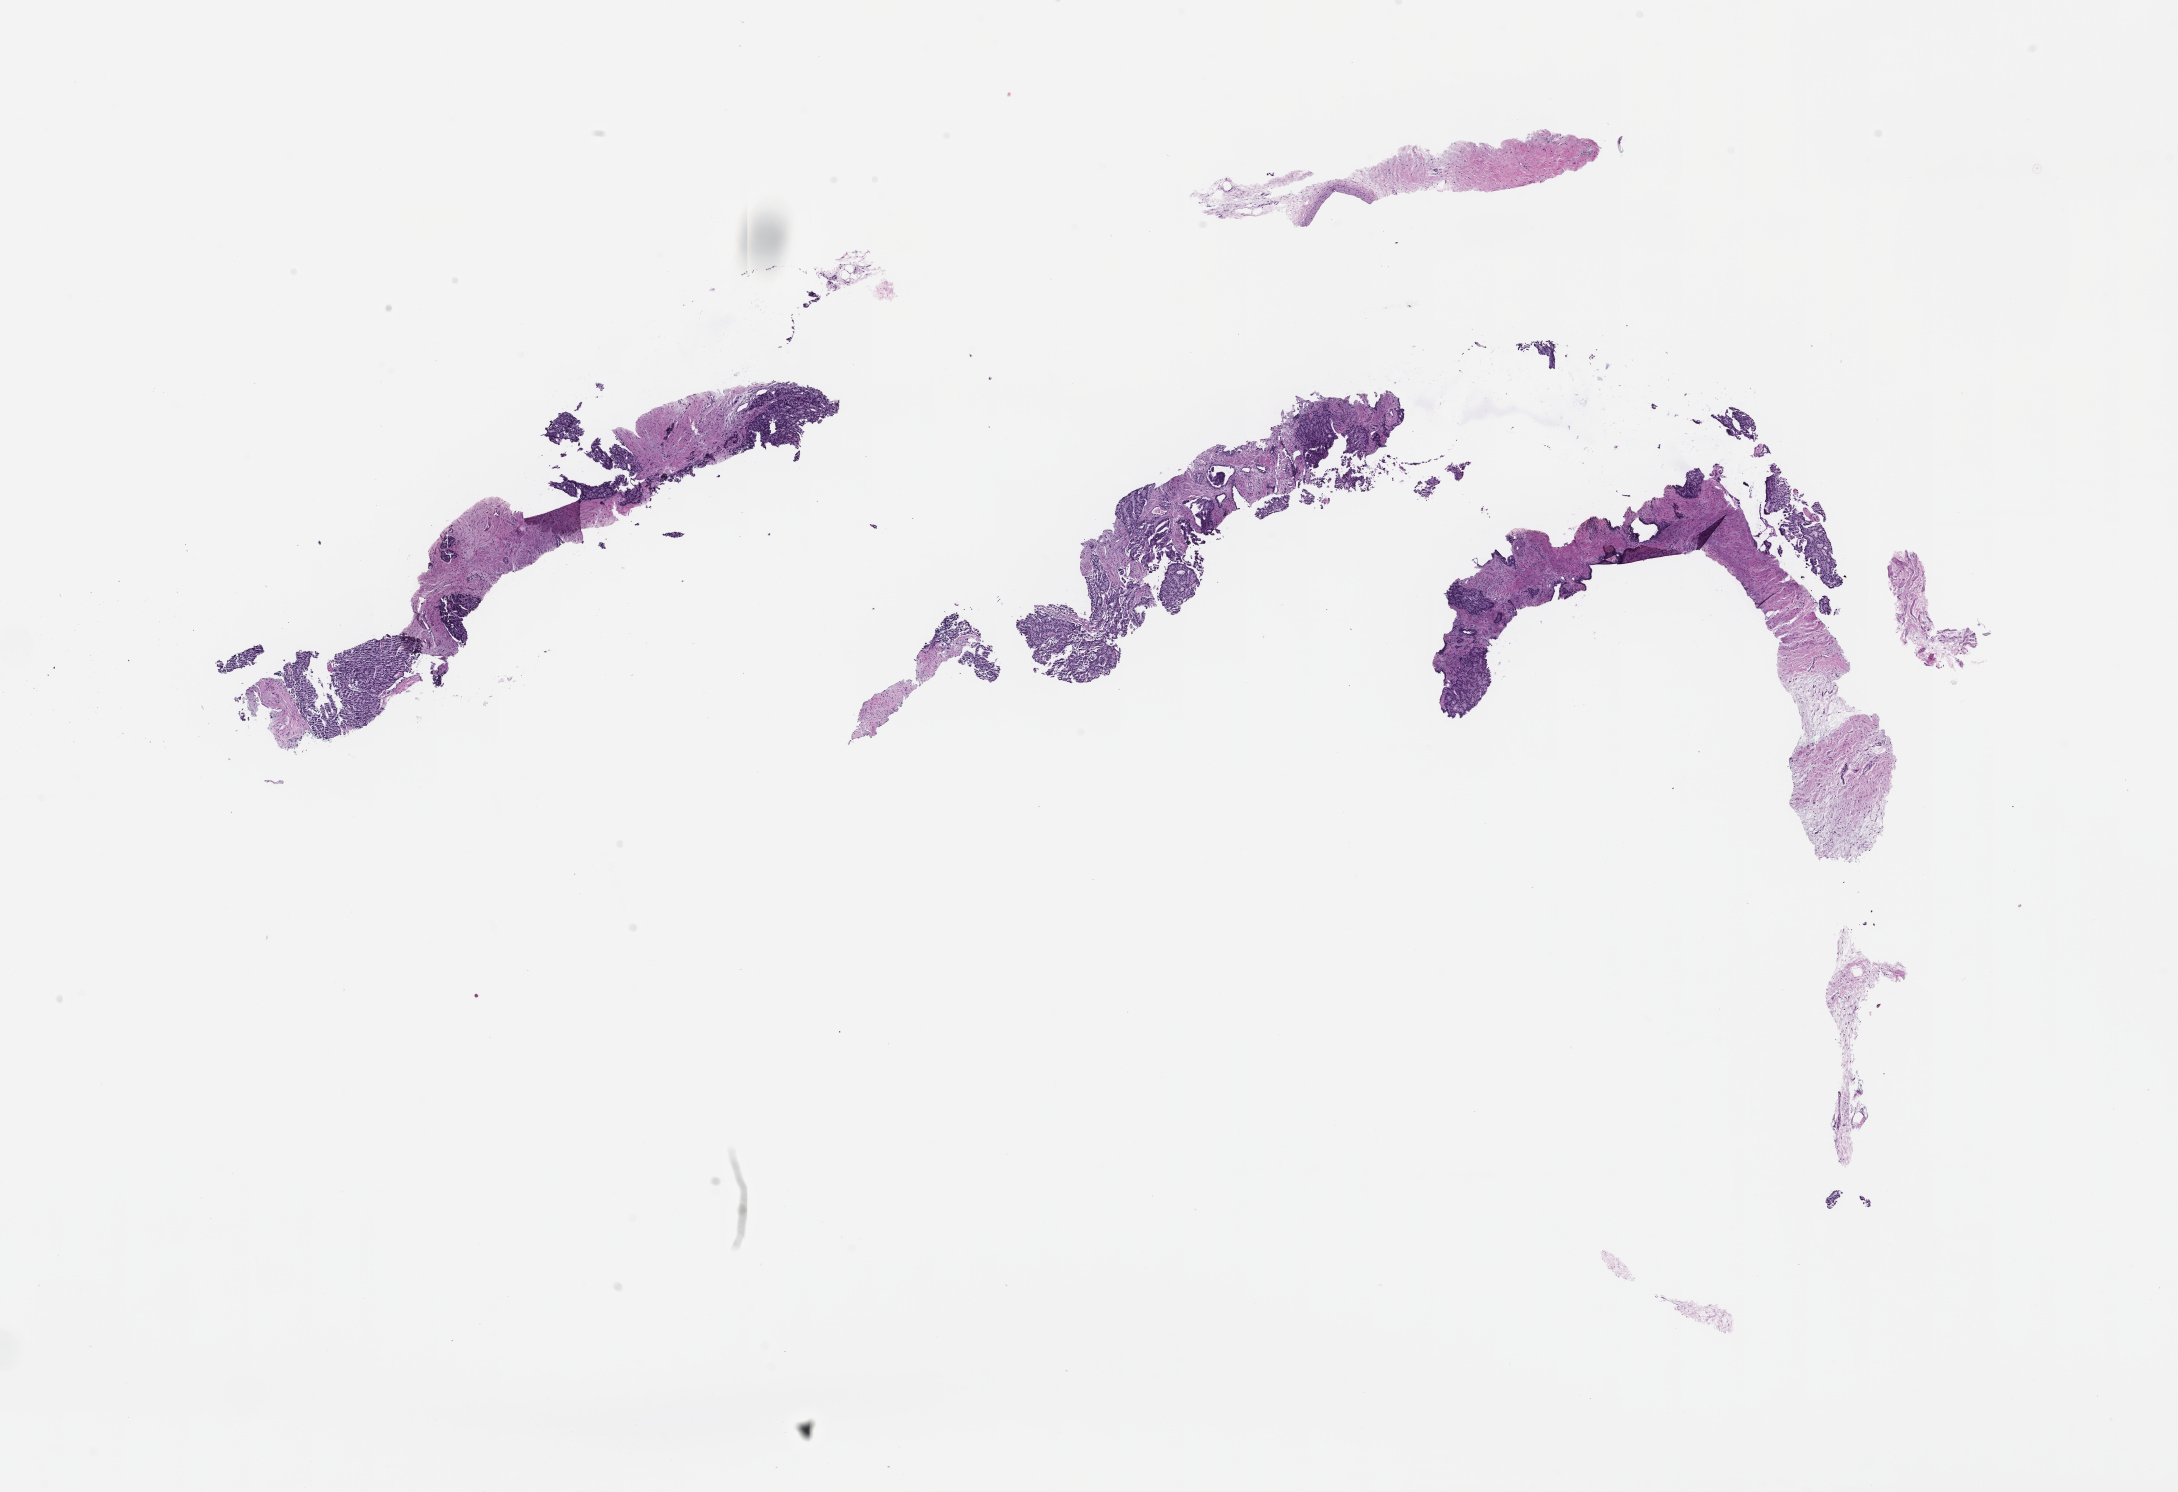
Digitized haematoxylin and eosin-stained section — low-resolution overview of the scanned area, about 17.6 x 12.0 mm; formalin-fixed, paraffin-embedded (FFPE) tissue; tissue site: prostate; archival tissue. Patient sex: male.
- this section: primary tumor
- diagnosis: Prostate Carcinoma